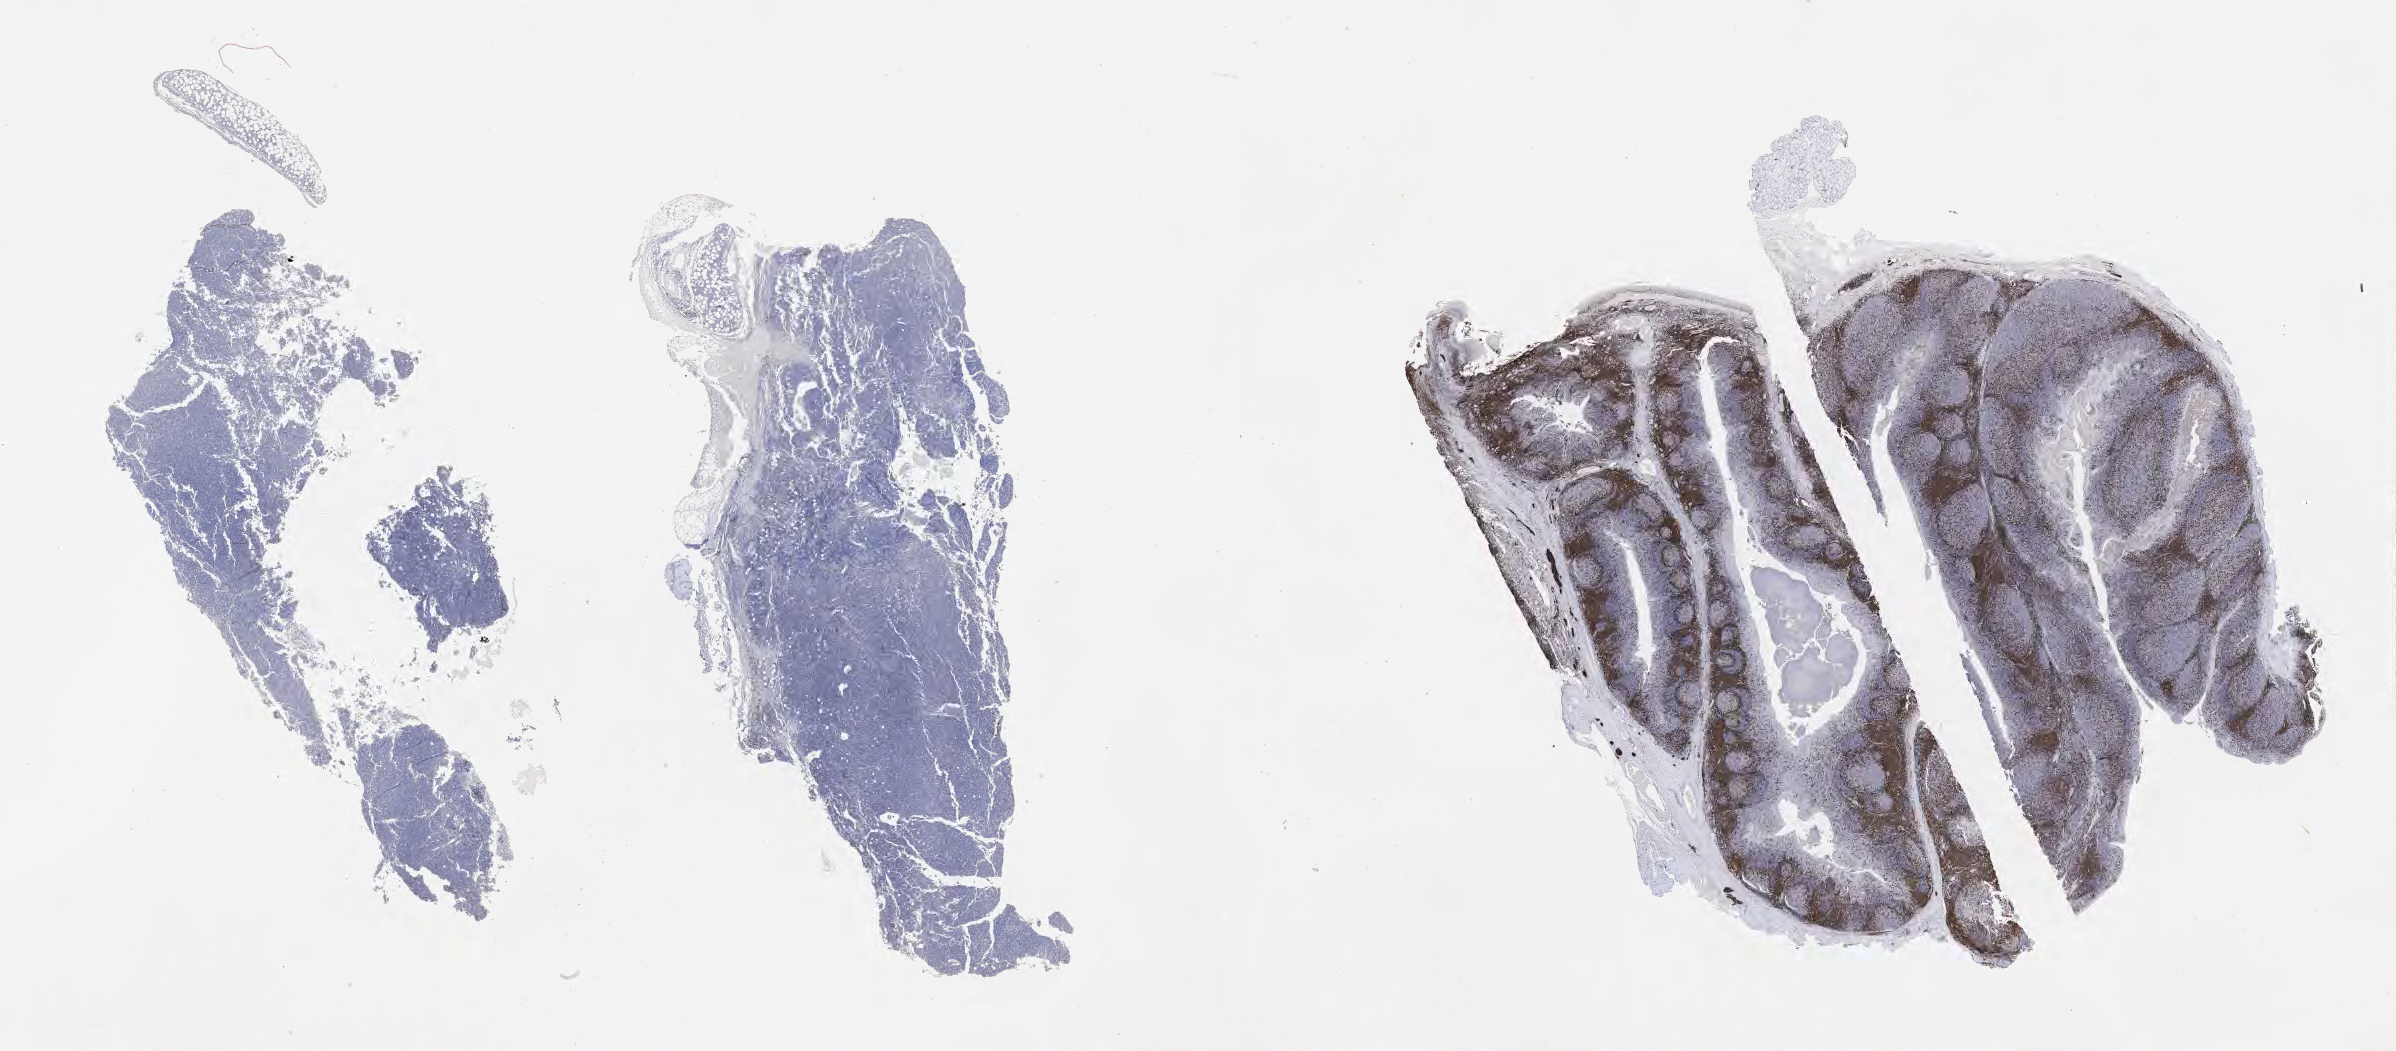
Immunohistochemistry (IHC) whole-slide image stained for CD3 — low-resolution overview of the scanned area, about 38.7 x 17.0 mm; specimen: tumor tissue. Patient female; aged 16.
Diagnosis: Burkitt lymphoma, NOS.